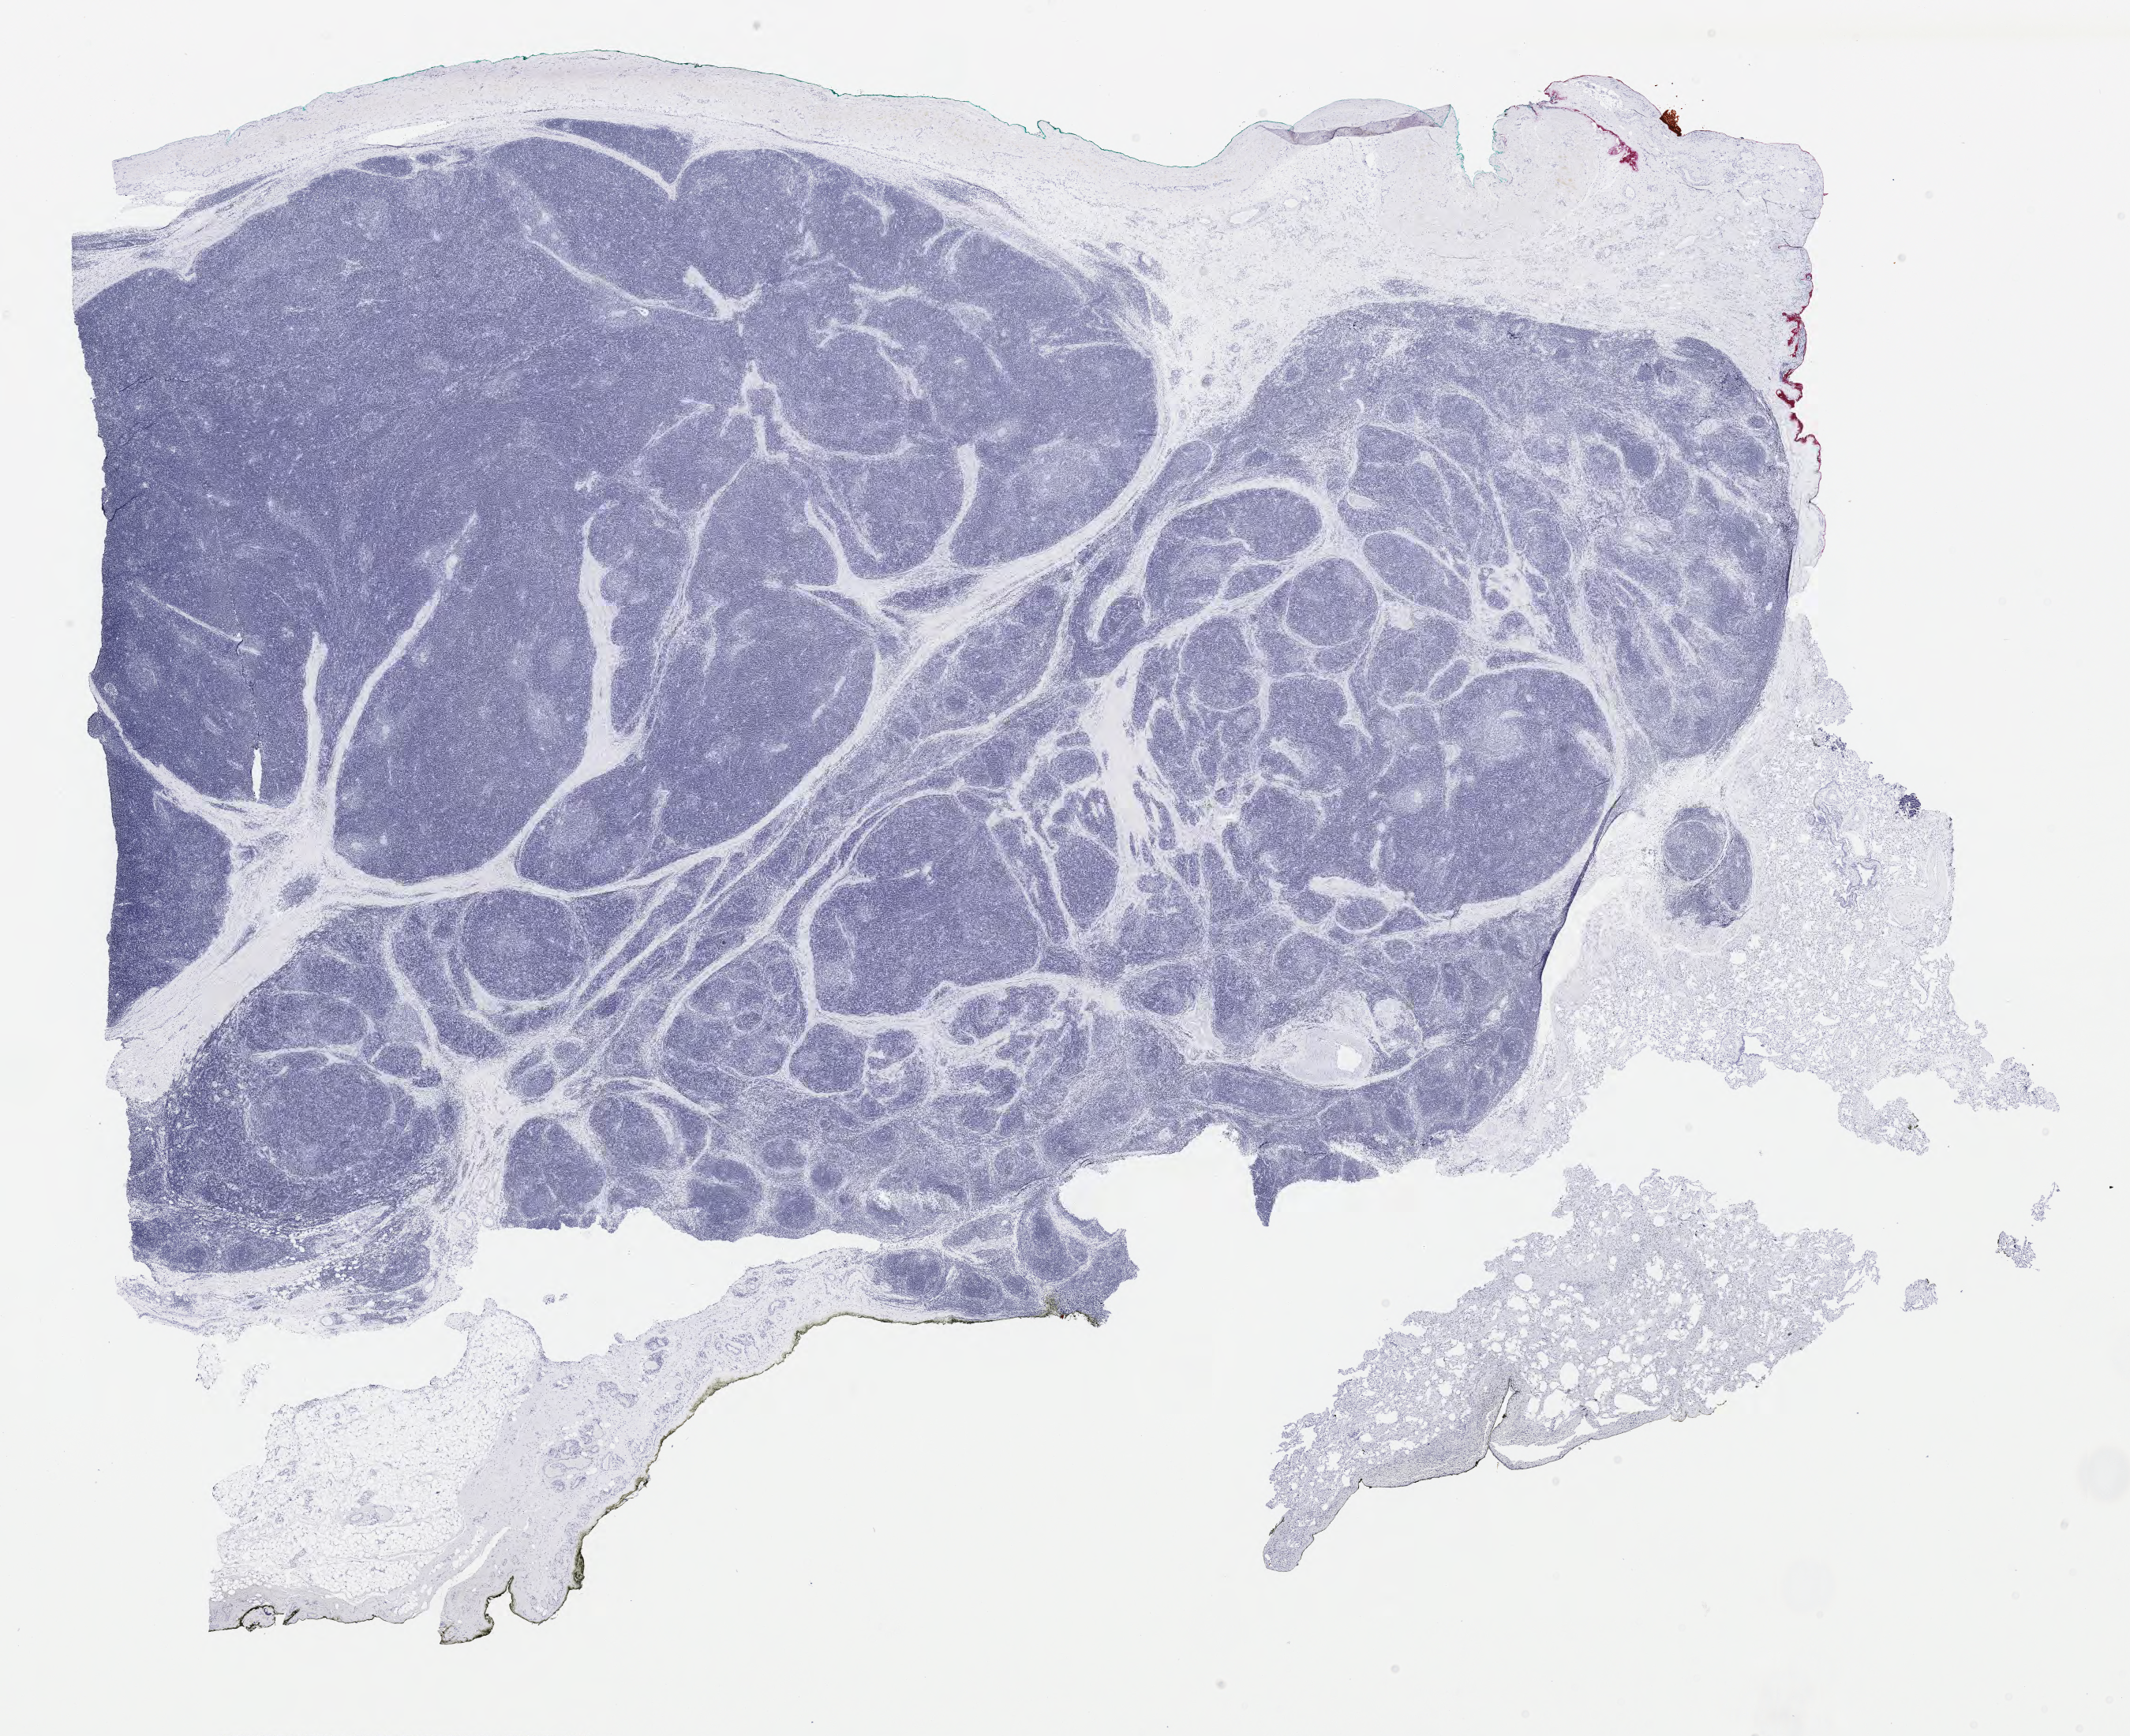
H&E-stained whole-slide image — a low-resolution overview of the entire scanned area, about 21.4 x 17.4 mm, FFPE section, thymus, primary tumour sample. Patient: female, age at initial diagnosis 57 years.
* pathologic diagnosis: Thymoma, type B1, NOS